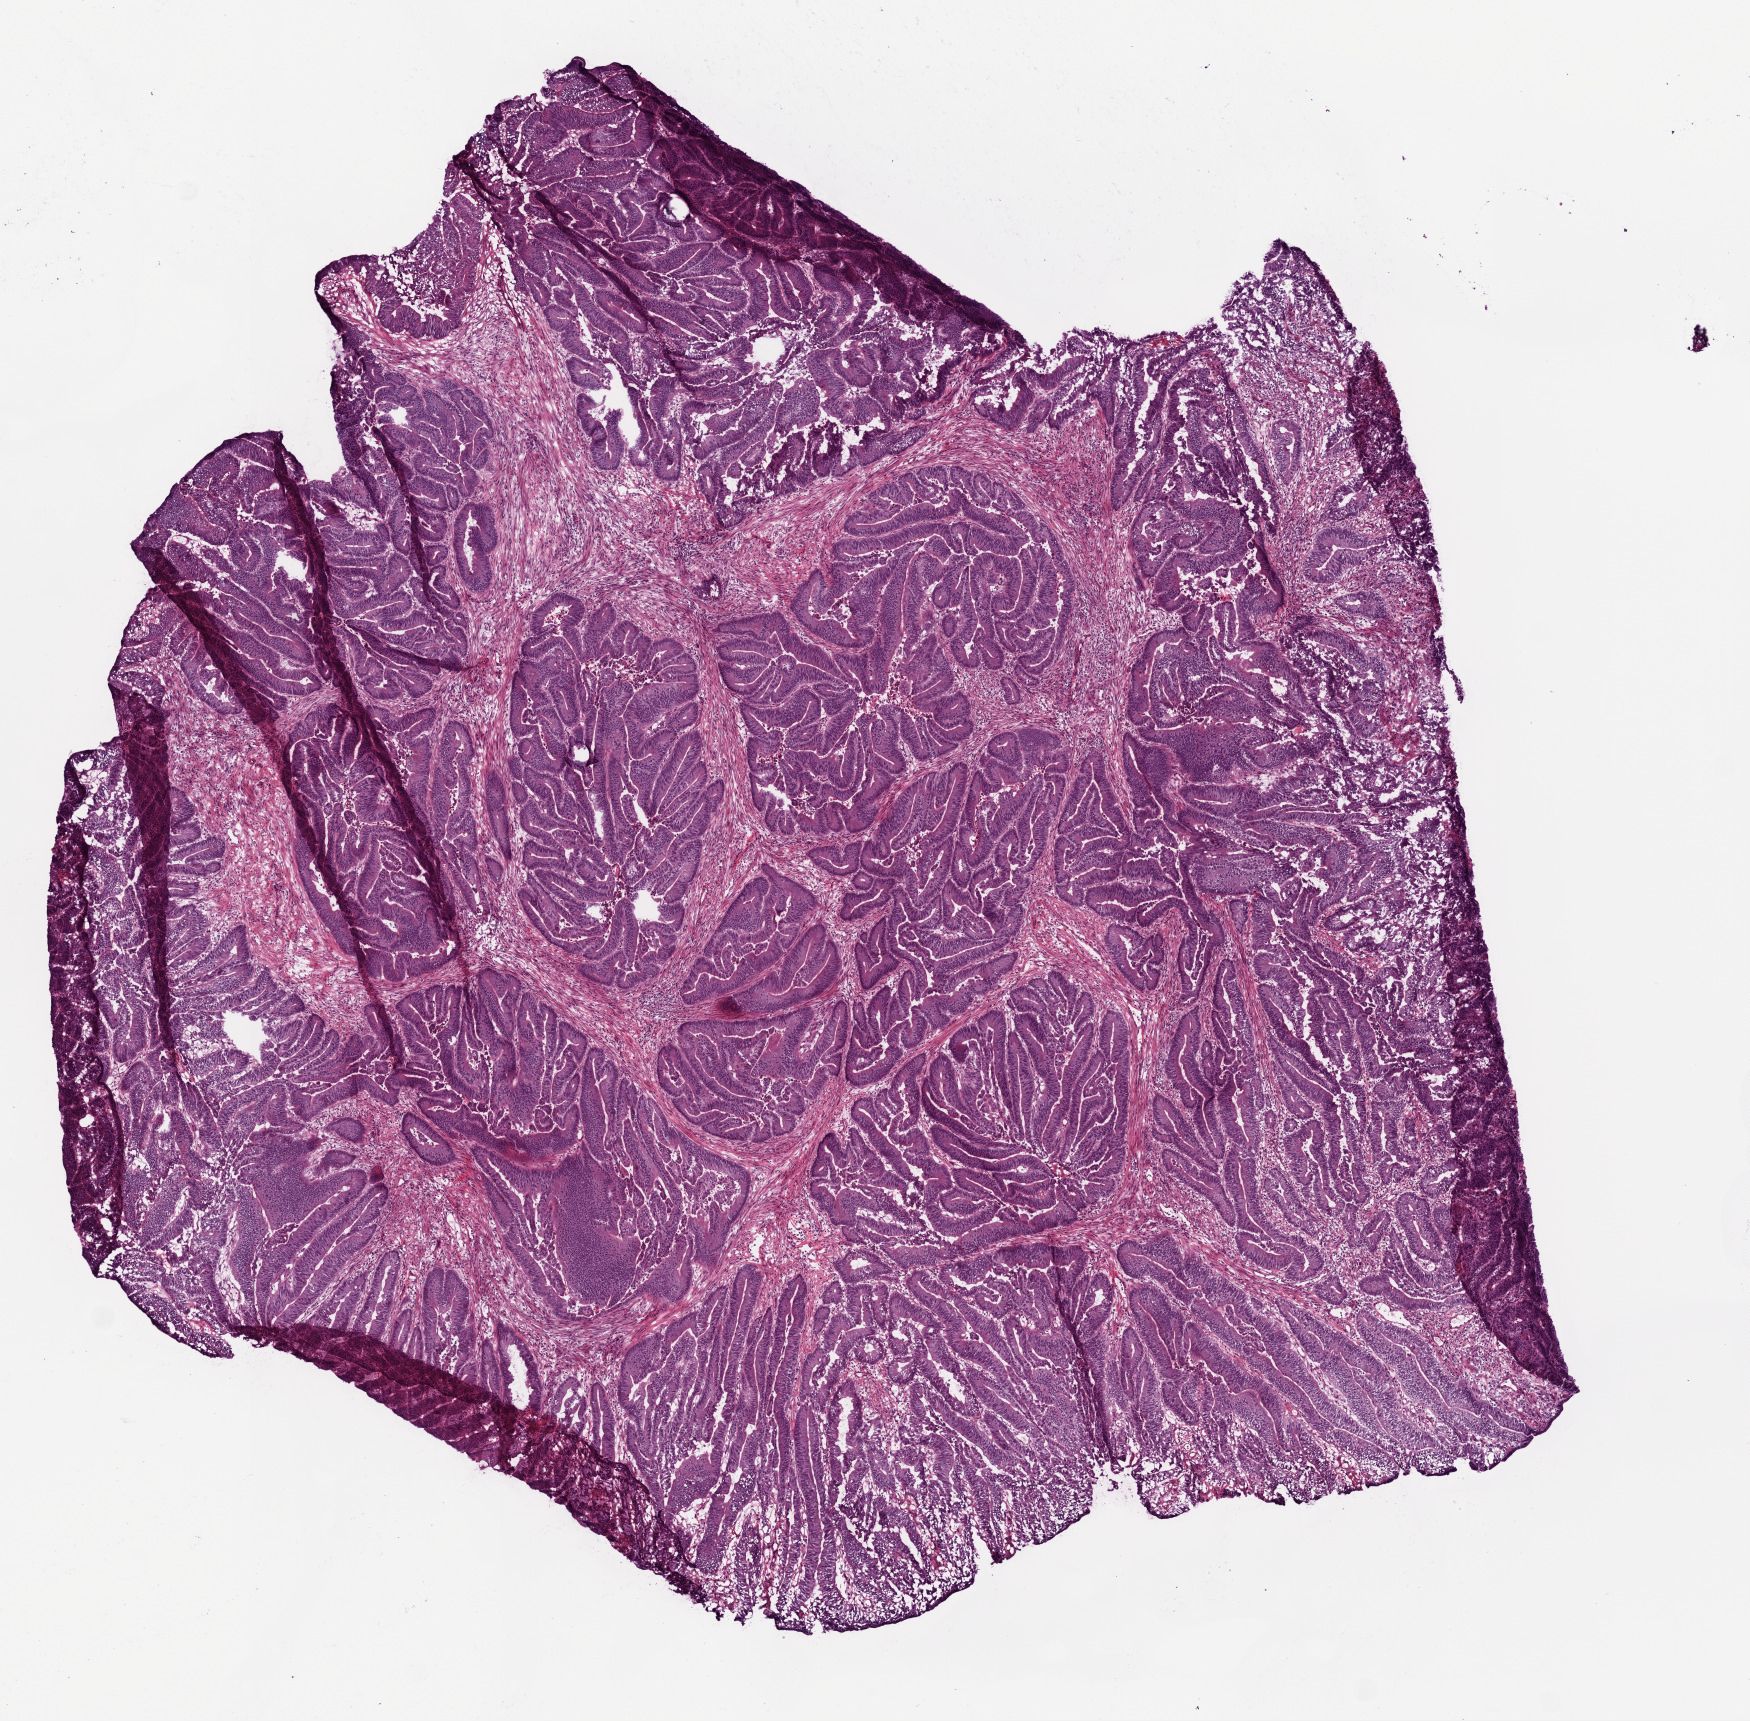
Digitized H&E tissue section (whole slide), a low-resolution overview of the entire scanned area, about 7.0 x 6.9 mm (slide scanned at 20x). Frozen section from the bottom of the tissue portion. Colon, primary tumour sample. Male patient; age at initial diagnosis 84 years. Composition of this section per pathologist review: tumour cells 80%, tumour nuclei 80%, normal cells 0%, stromal cells 20%, necrosis 0%.
Histologic diagnosis: Adenocarcinoma, NOS. AJCC pathologic stage: II. Lymph nodes positive (case pathology): 0 of 24 examined.